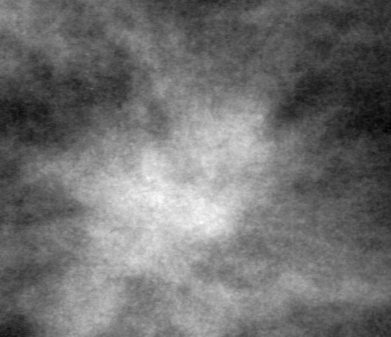
Cropped region of a digitized screen-film mammogram centred on a radiologist-marked abnormality; left breast; CC view.
Finding: mass, shape architectural distortion, margins spiculated; BI-RADS assessment category 5; subtlety rating 2 on a 1 (subtle) to 5 (obvious) scale; pathology result (as recorded, not read from the image): malignant.